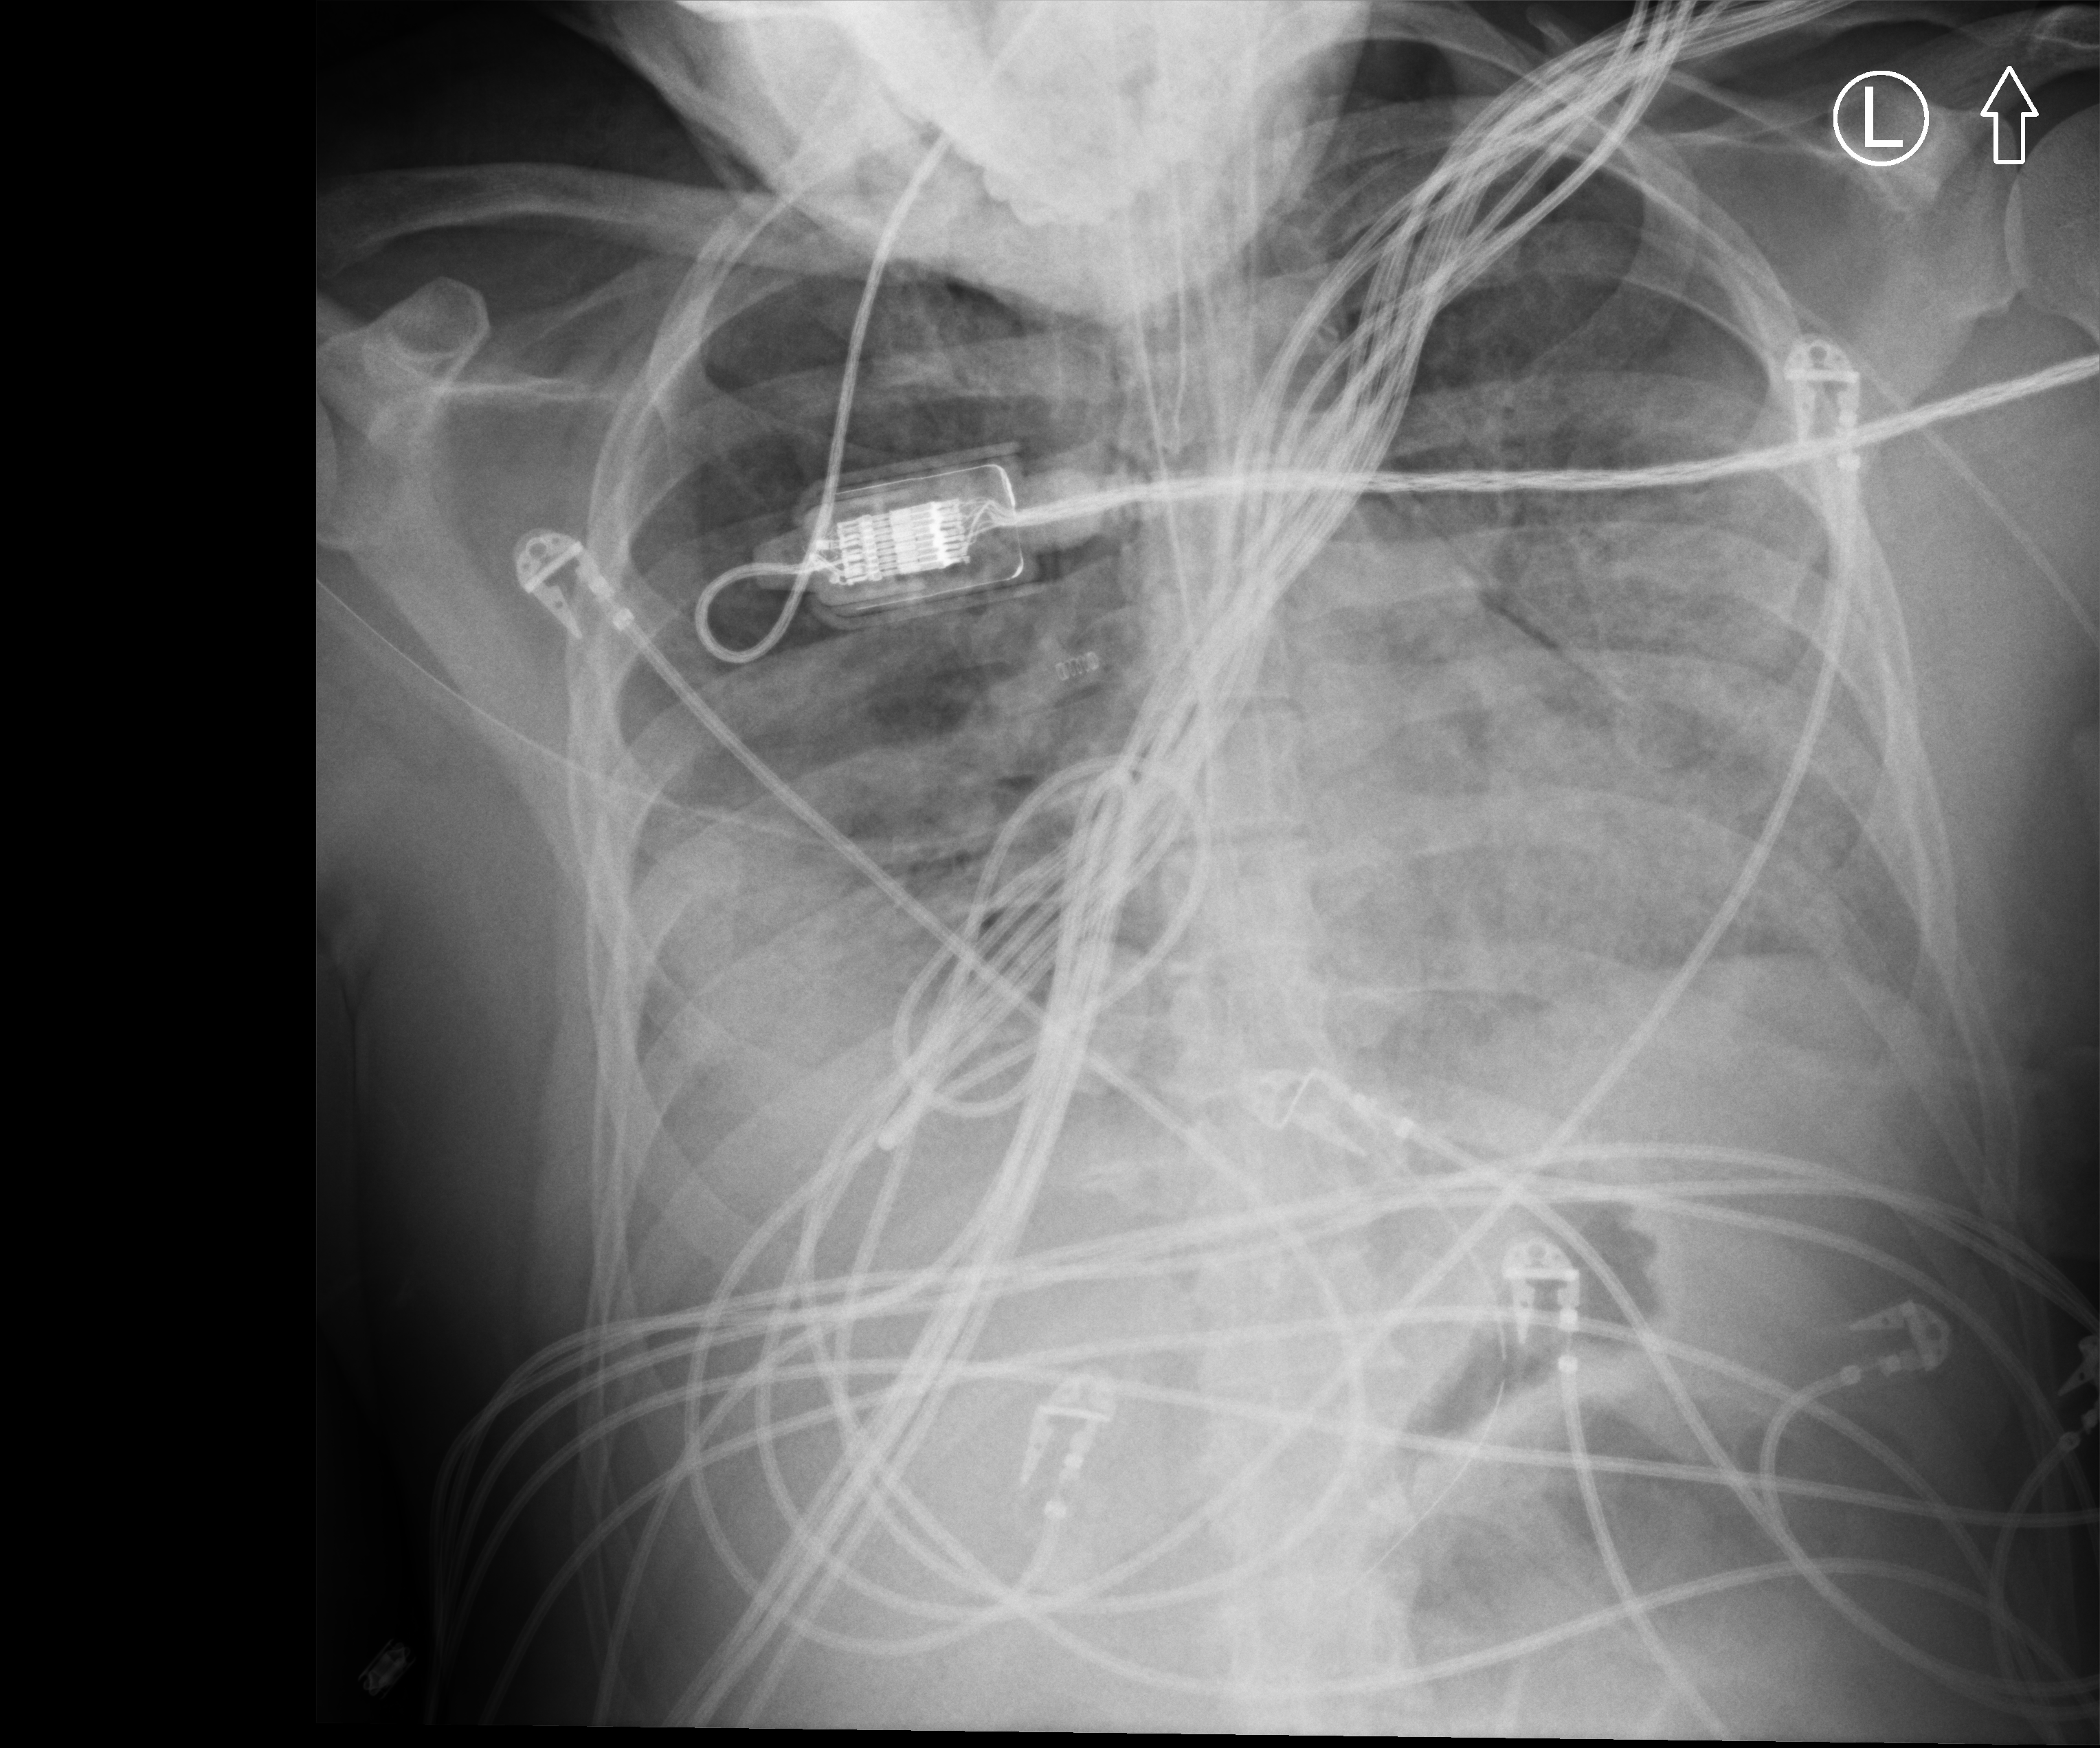
Bedside chest radiograph (computed radiography), anteroposterior (AP) projection. Male patient hospitalised with COVID-19, age 18–59 years.
From the hospital-stay record, not from the radiograph (when in the stay this image was taken is not recorded): mechanically ventilated during this hospital stay: yes; other chronic lung disease (admission record): no.